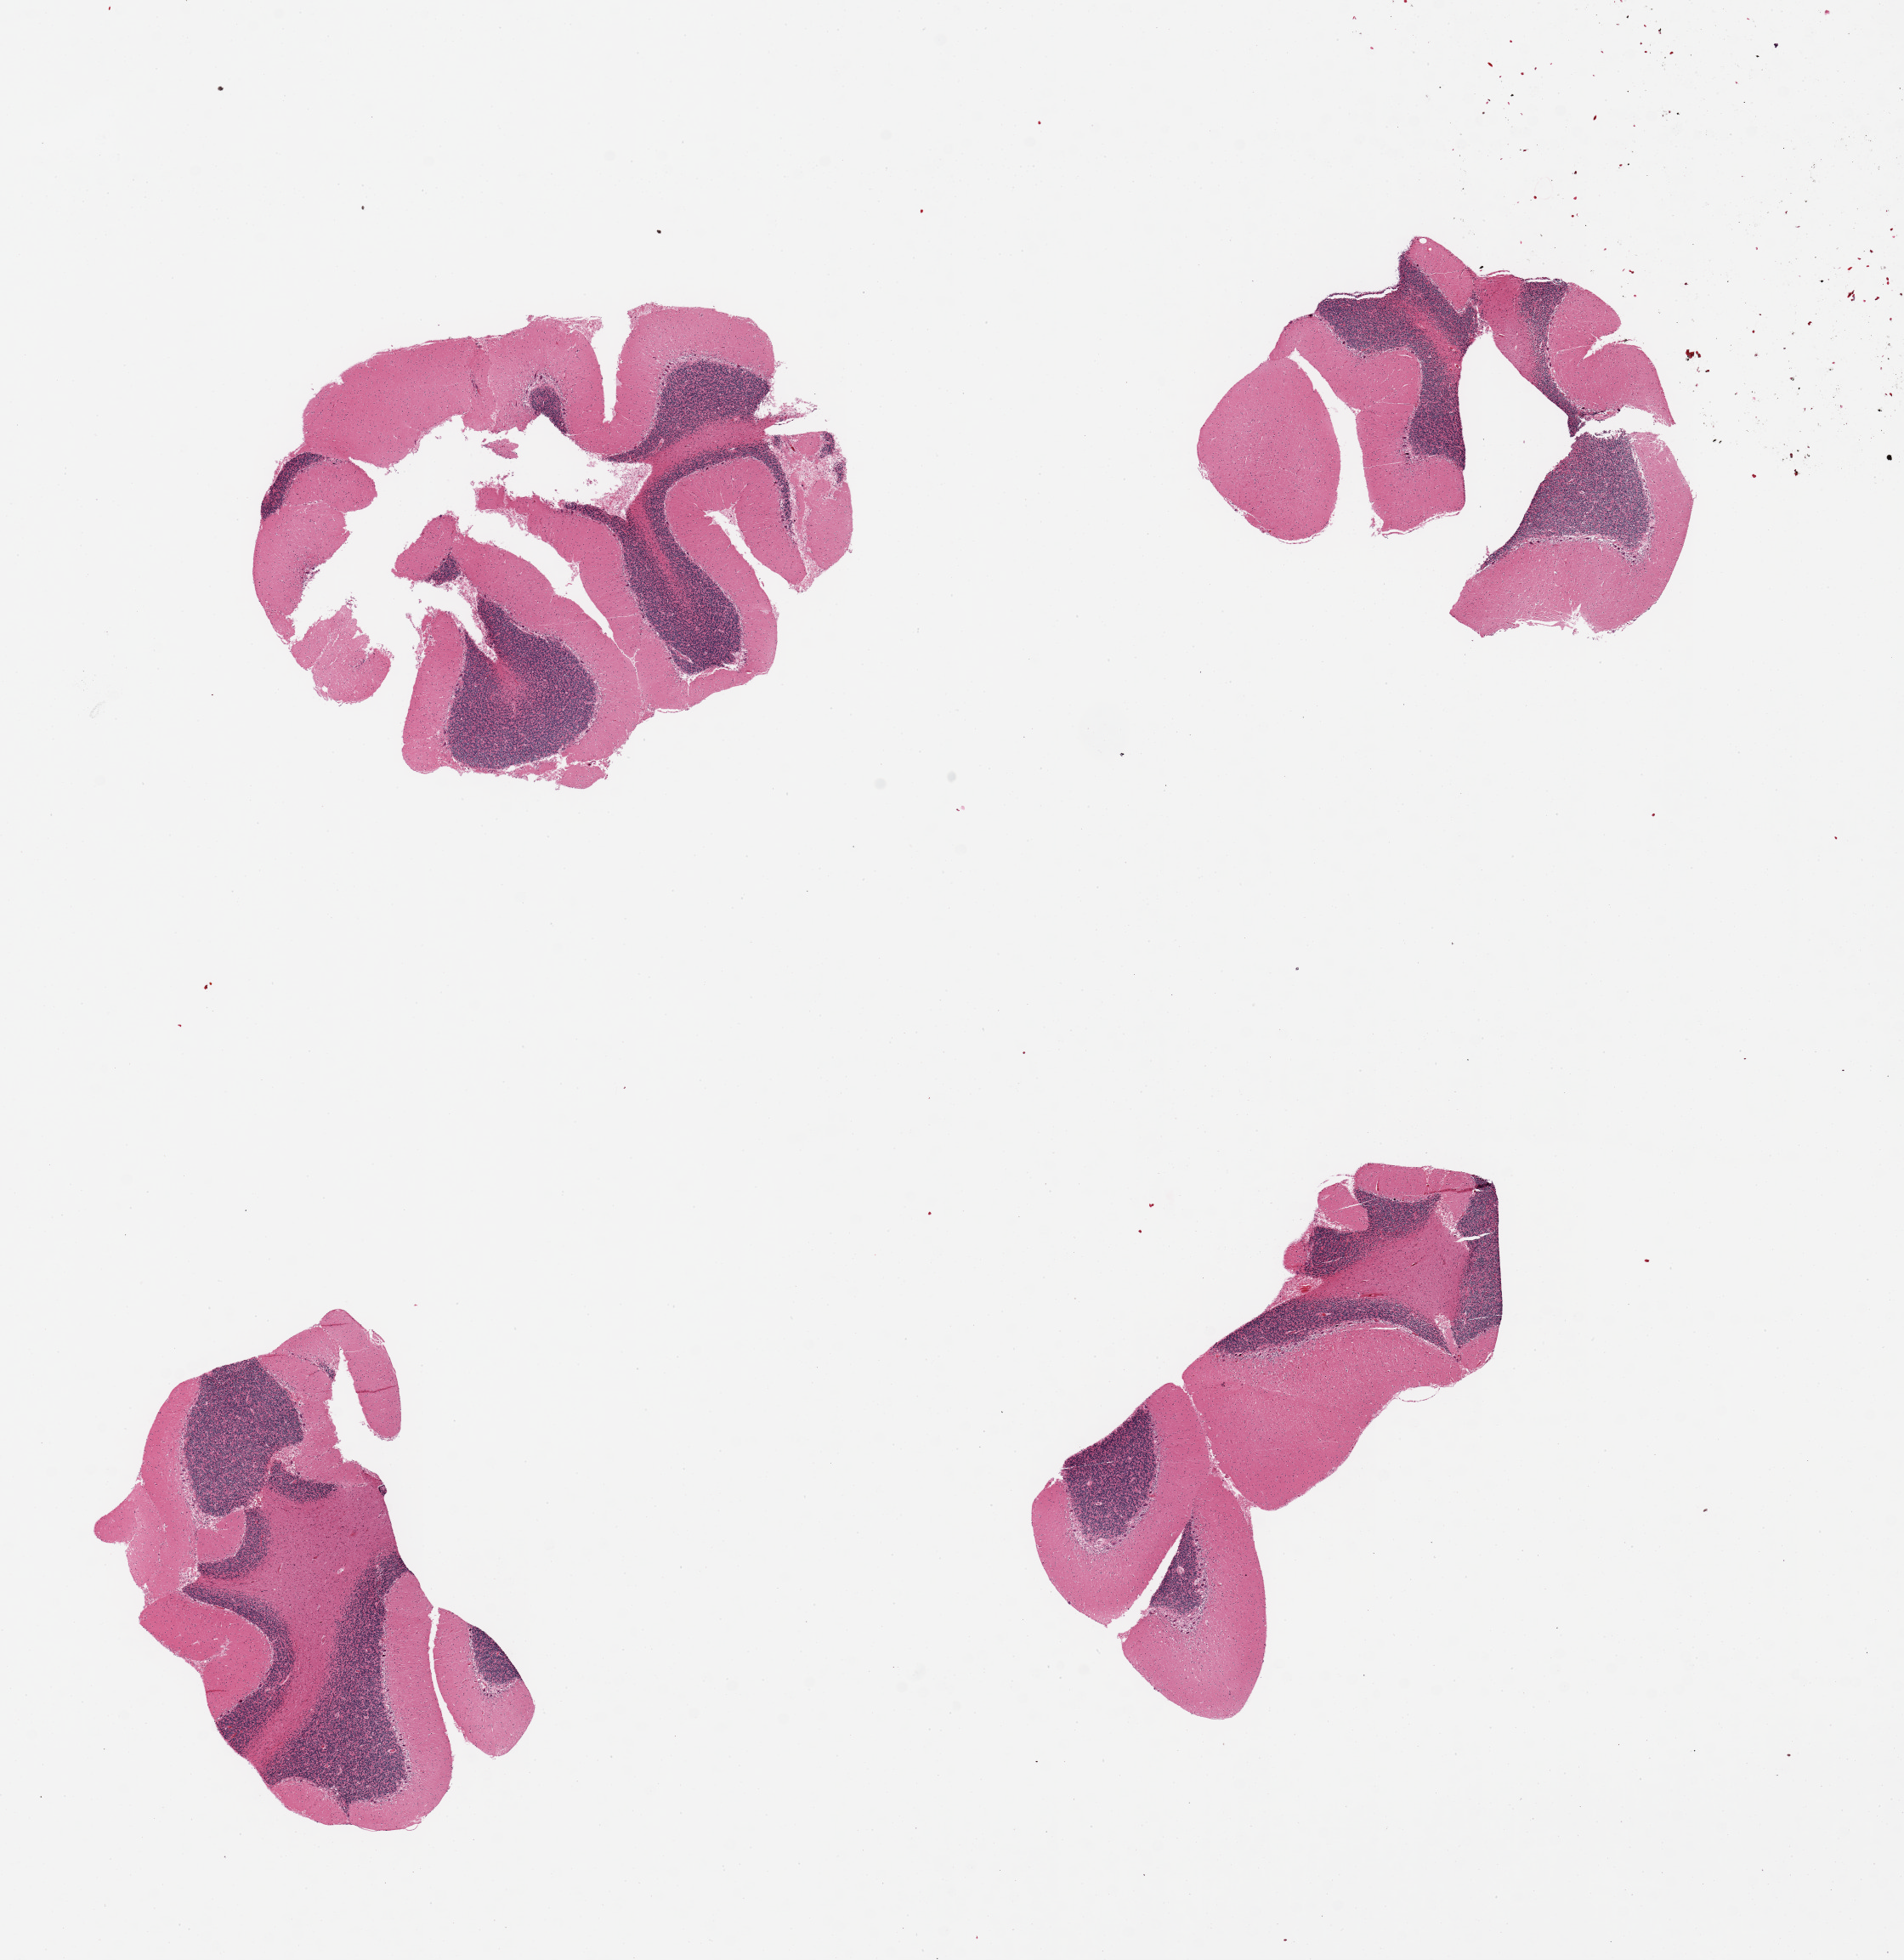
Haematoxylin and eosin whole-slide image — whole scanned area (about 17.7 x 18.2 mm) shown as a low-resolution overview; PAXgene-fixed, paraffin-embedded tissue; section of cerebellum (target tissue); tissue donor sample. Donor: male.
Pathologist's review note for this sample: 4 pieces. Good Purkinje cells.